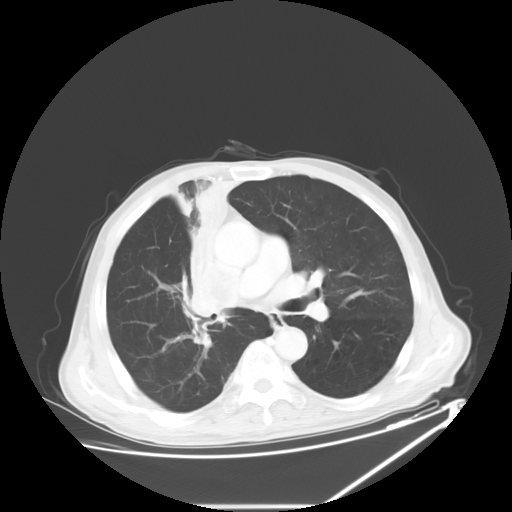
Chest CT, one axial slice; slice 36 of 60 in the series (ordered by position); reconstruction kernel STANDARD; 120 kVp; lung window (W 1500 / L -600 HU); 5 mm slice thickness; 512 × 512 image matrix, field of view 410 × 410 mm. Patient: male, 73 years. Case-level facts recorded for this patient, not image findings: clinical TNM (as recorded): T2a N1 M0.
Structures marked on this image (bounding box drawn by a radiologist):
- lung tumour (recorded histology: squamous cell carcinoma): bounding box [x1, y1, x2, y2] px = [171, 171, 243, 330]